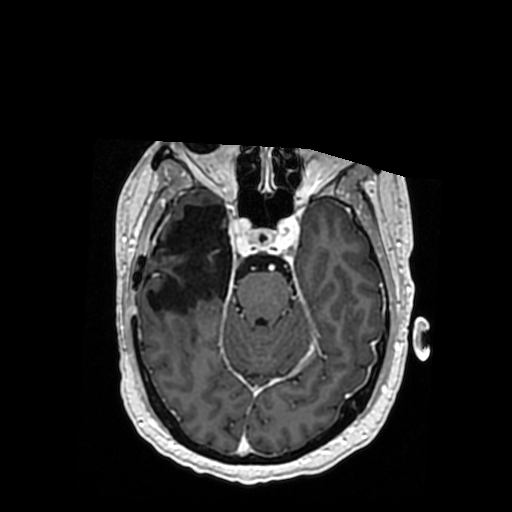
Brain MRI from a brain-tumour surgery series, one axial slice. Slice 229 of 364 in the series (ordered by position). T1-weighted post-contrast. 0.5 mm slice thickness. 512 × 512 image matrix, field of view 260 × 260 mm. From the clinical record (not read from this slice): histopathology: Oligodendroglioma; WHO grade: 3; IDH mutation: yes.
Annotated regions visible in this slice (outlined manually by an expert reader):
- previous resection cavity: box from (x=147, y=205) to (x=232, y=313) px